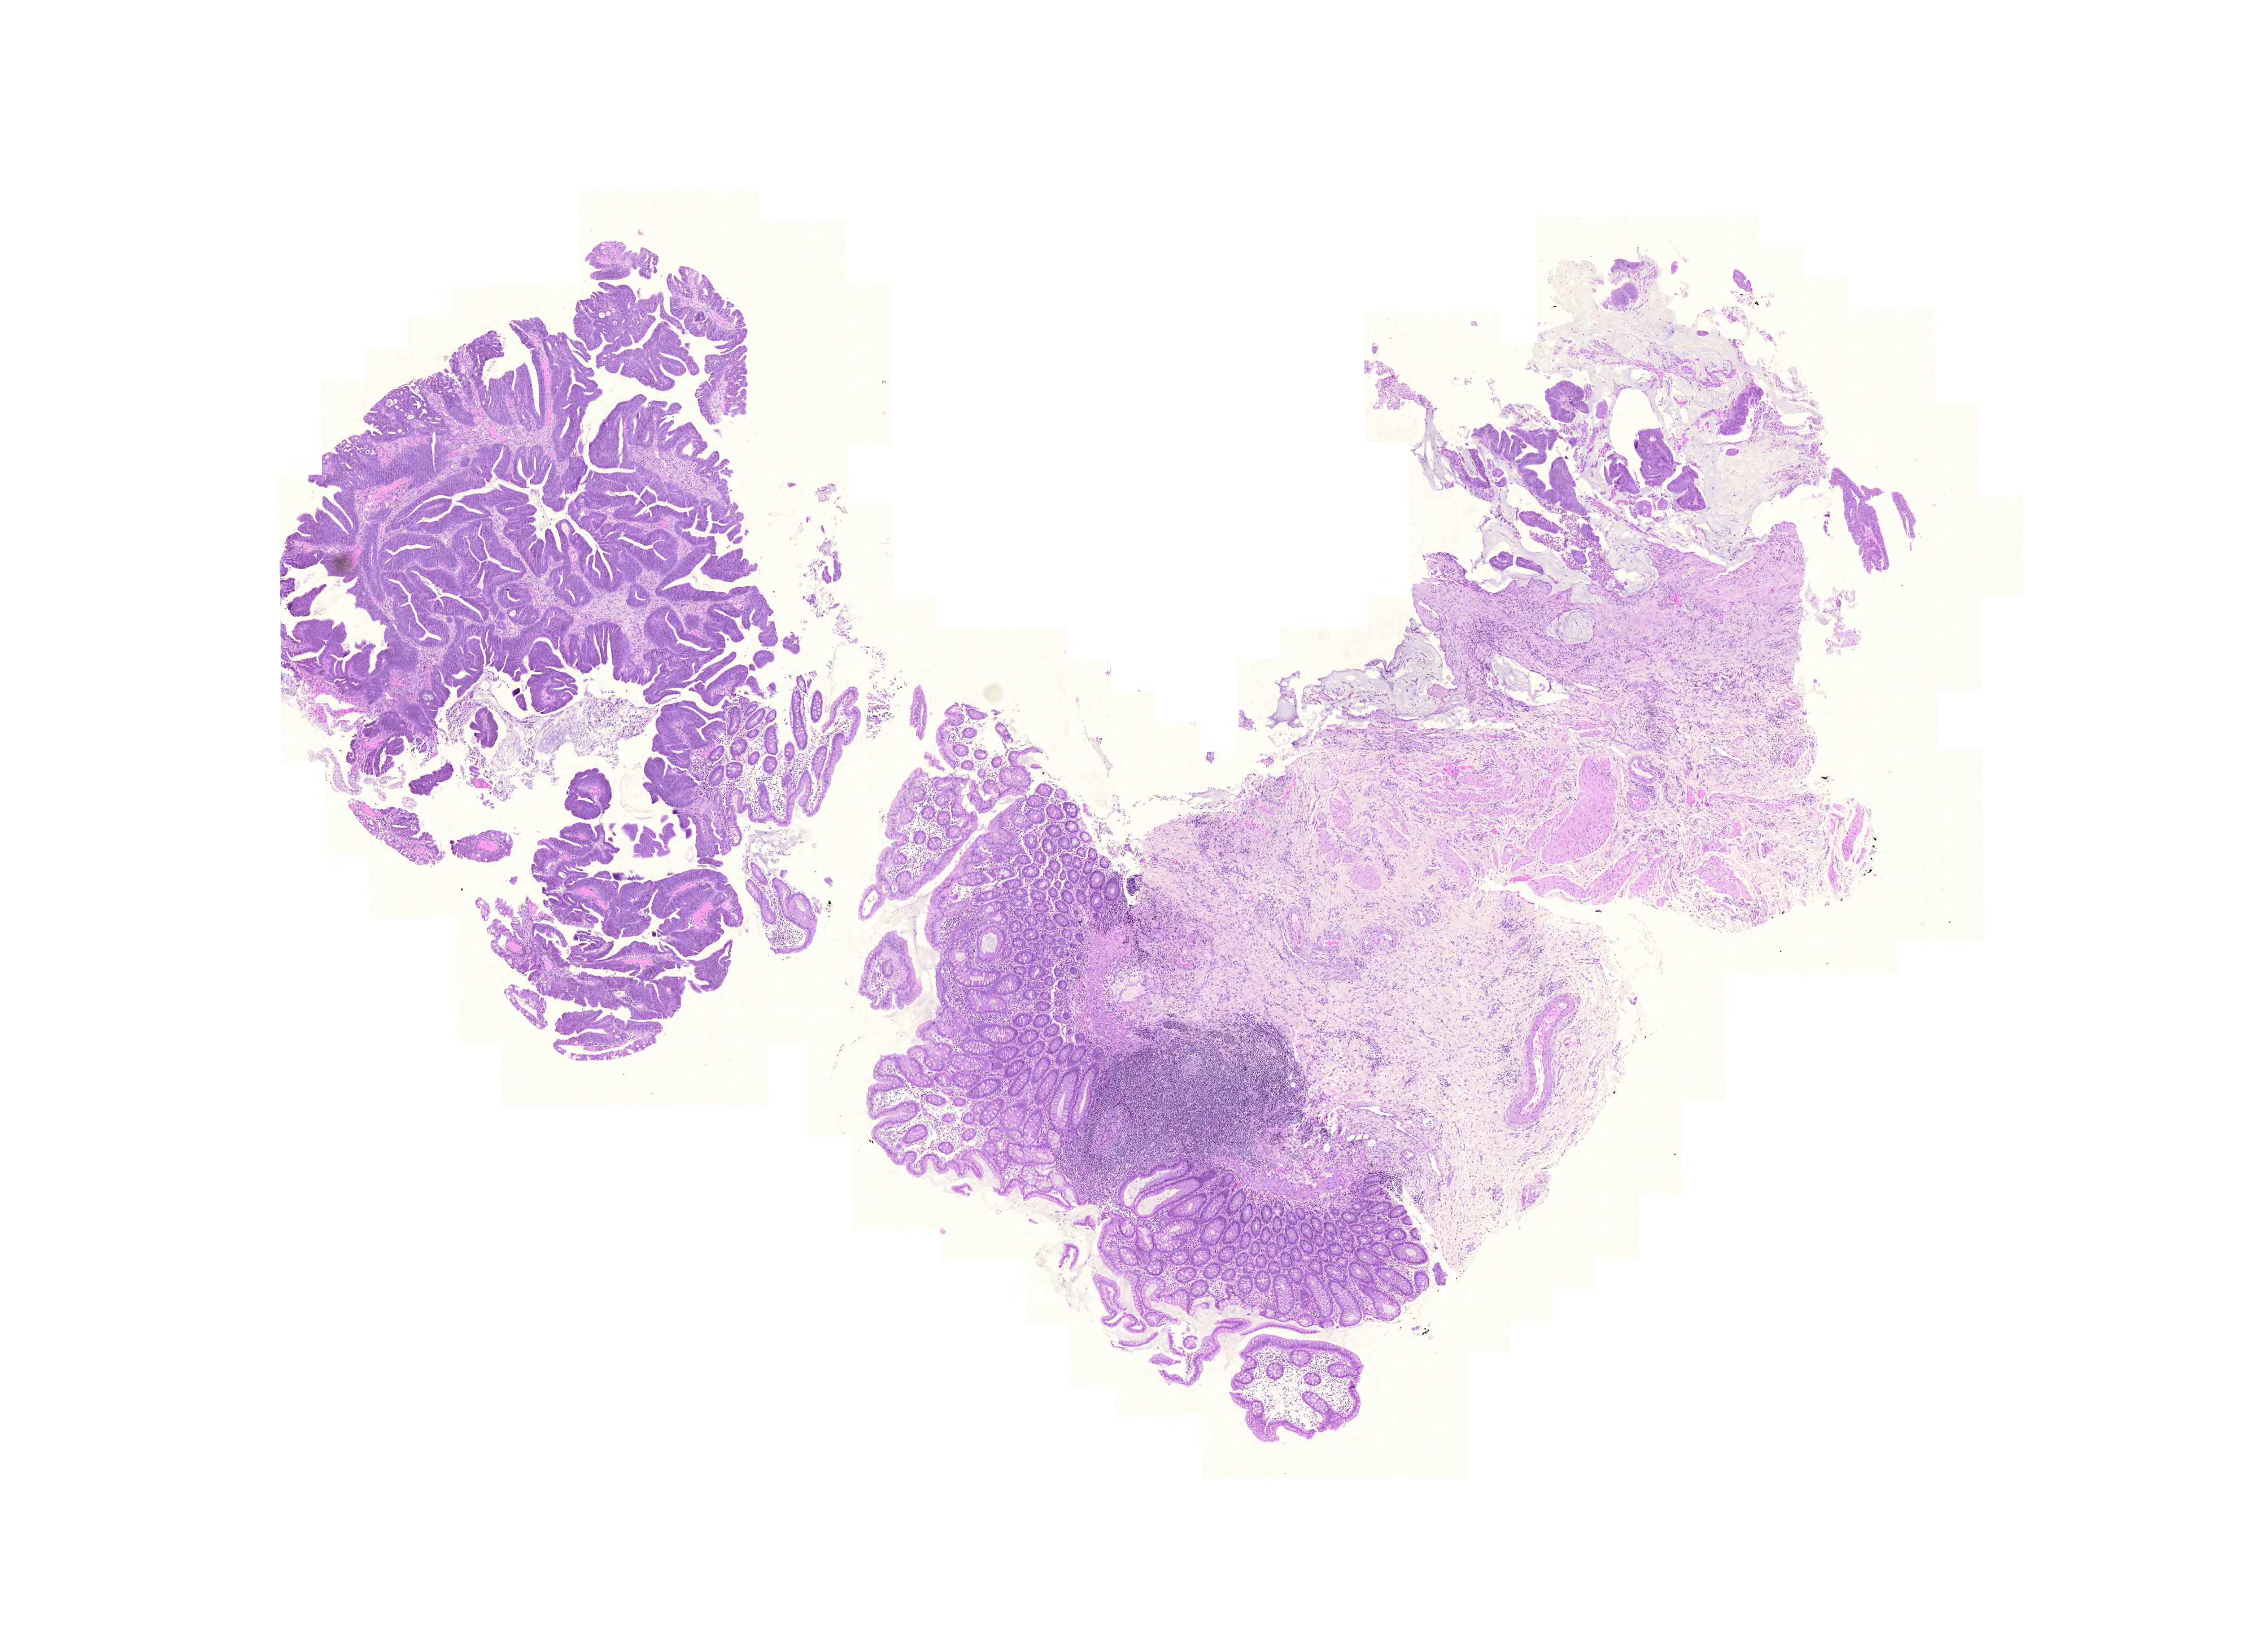
Digitized H&E-stained tissue section (whole slide) — whole scanned area (about 14.9 x 10.8 mm, from a 20x scan) shown as a low-resolution overview; FFPE section; sample: primary tumour, colon. Male patient; age at initial diagnosis 71 years.
* AJCC pathologic stage: II
* histologic diagnosis: Adenocarcinoma, NOS (cecum)